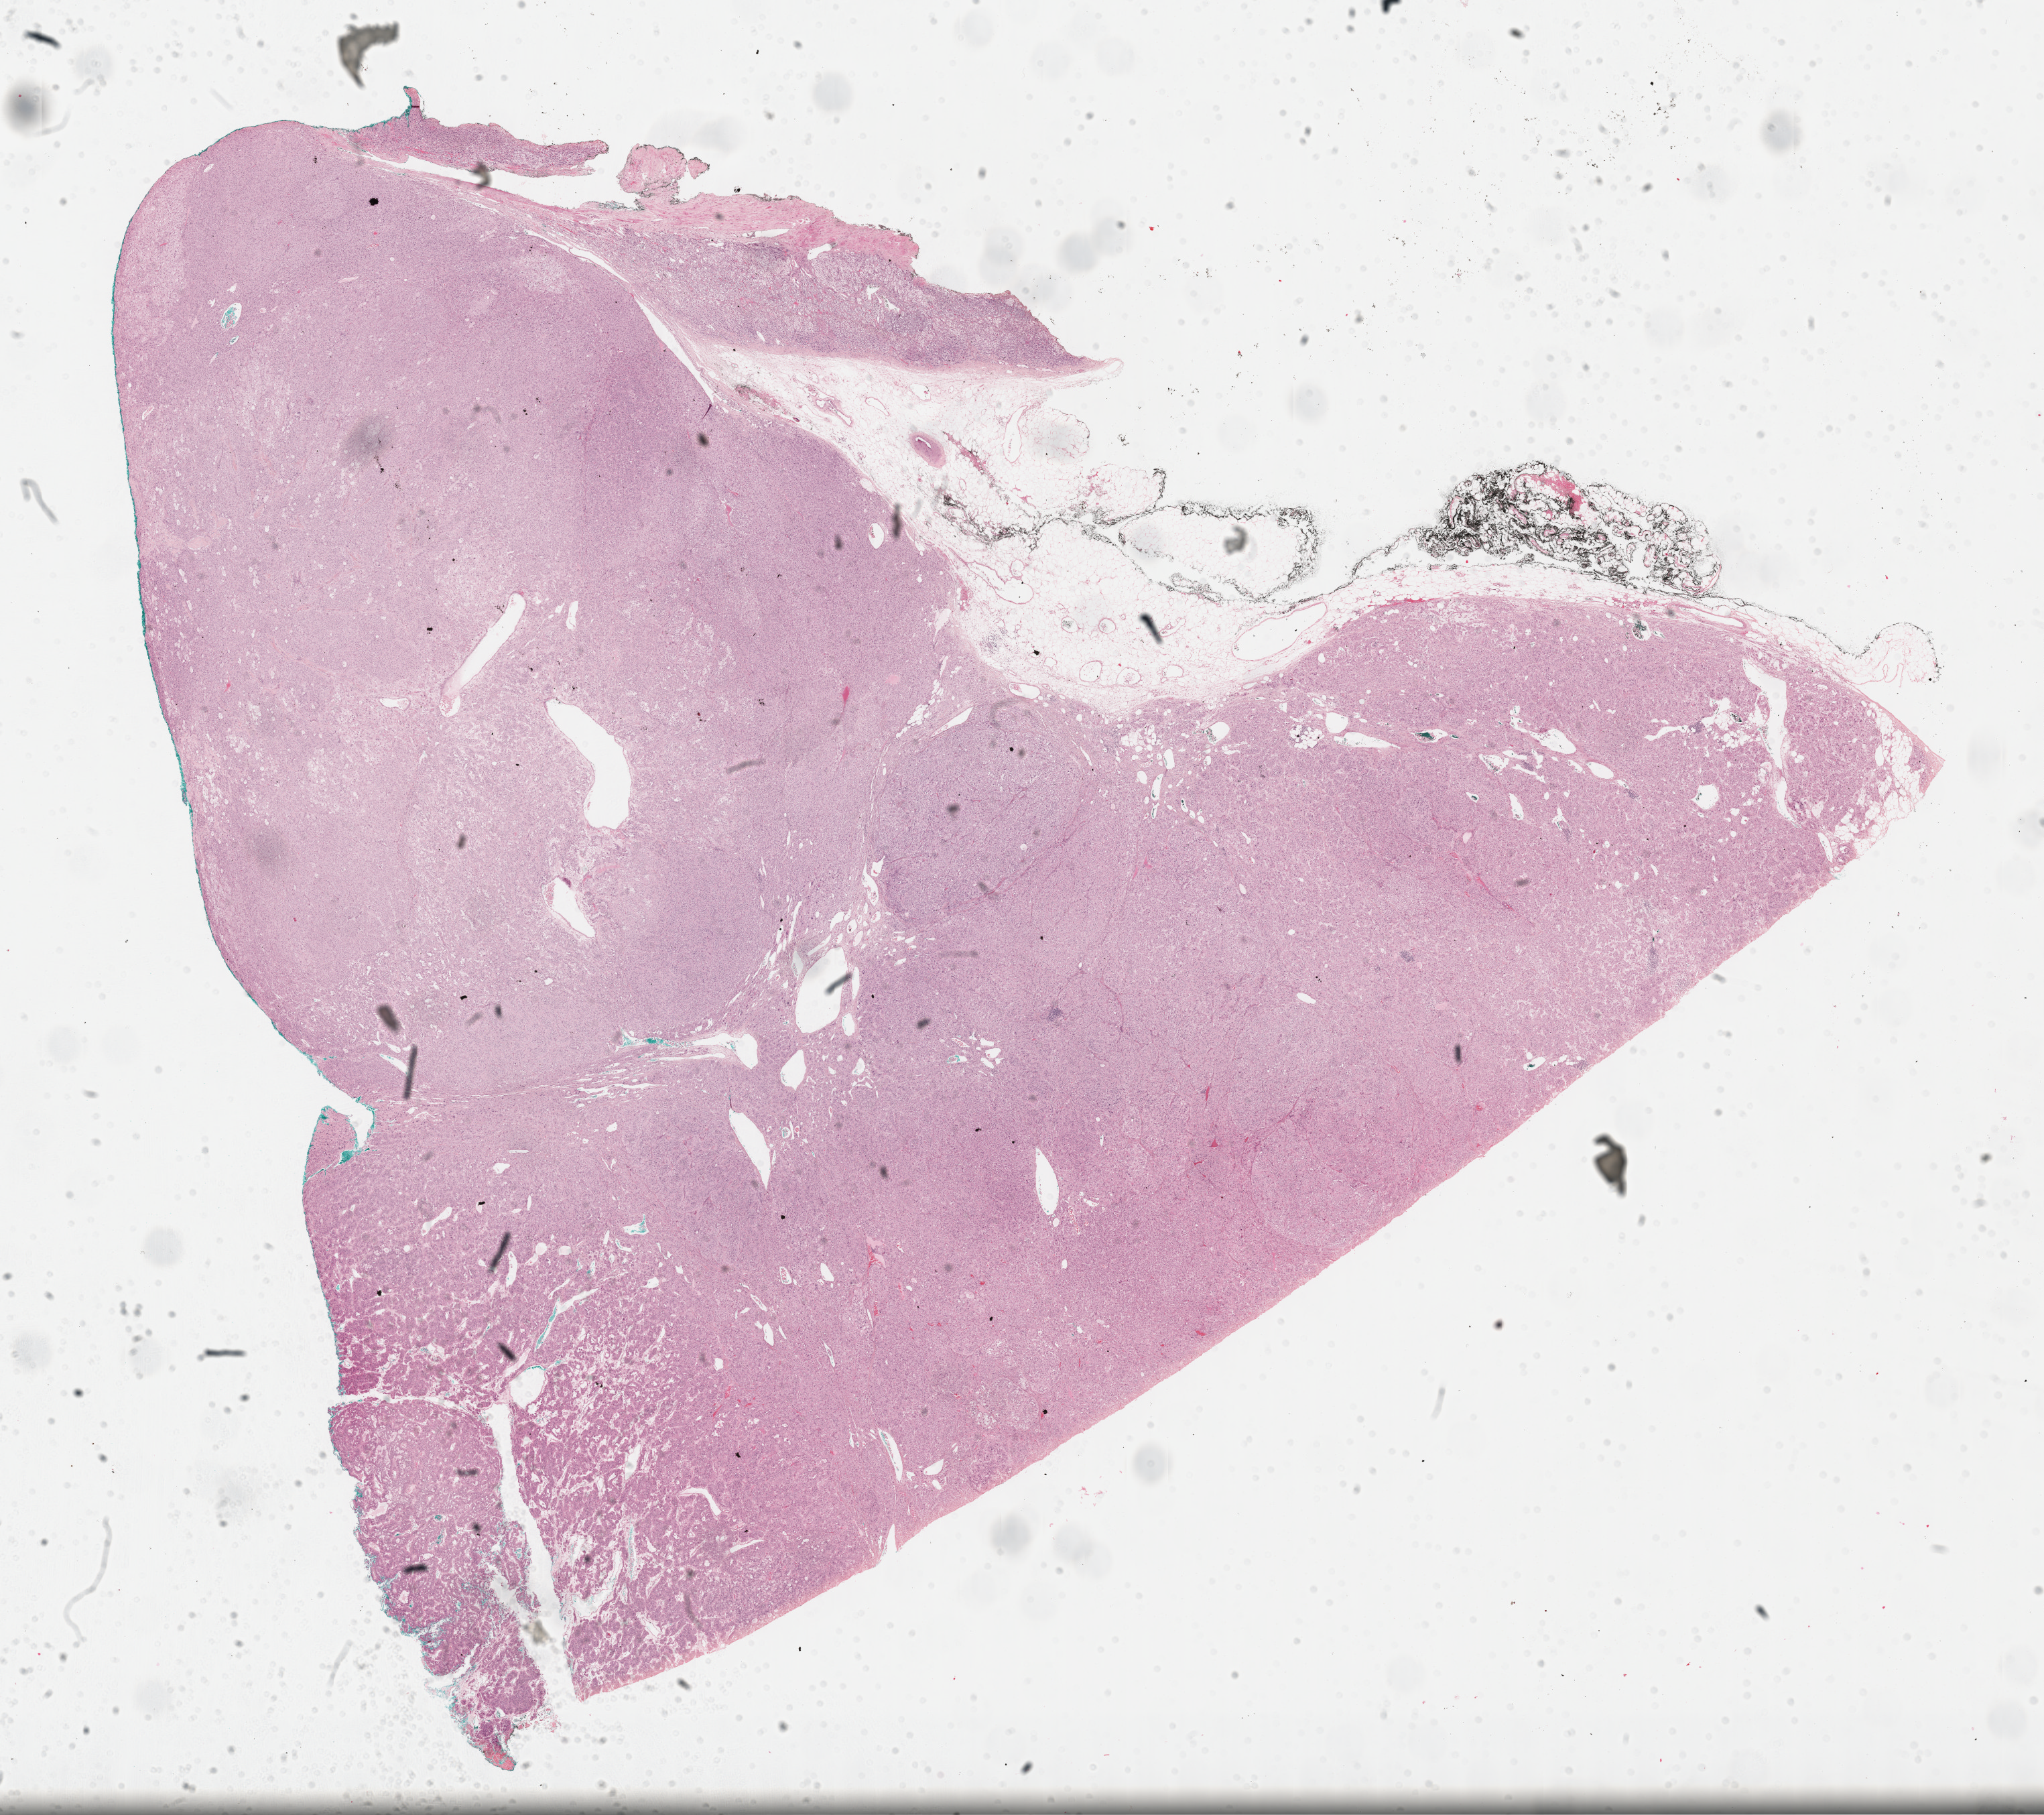
Digitized H&E-stained tissue section (whole slide), low-resolution overview of the scanned area, about 24.7 x 21.9 mm (slide scanned at 40x). Formalin-fixed paraffin-embedded (FFPE) diagnostic section. Adrenal cortex, primary tumour sample. Female patient; age at initial diagnosis 69 years.
* pathologic diagnosis: Adrenal cortical carcinoma (cortex of adrenal gland)
* laterality: left